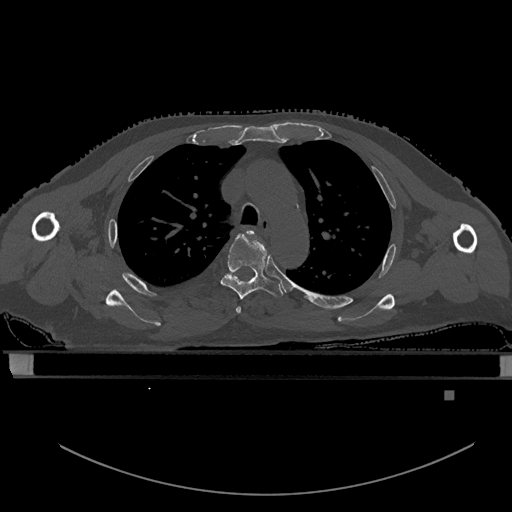
CT including the spine, one axial slice. Slice 409 of 969 in the series (ordered by position). Bone window (W 1800 / L 400 HU). 512 × 512 image matrix. Male patient, age 82 years. From the clinical record (not read from this slice): primary cancer: prostate; vertebrae with lytic lesions (as recorded): T11, T9, T8, T2.
Structures marked on this image (semi-automatic segmentation, software-assisted and operator-edited):
- T3 vertebra: bounding box [x1, y1, x2, y2] px = [235, 230, 254, 314]
- T4 vertebra: [220, 234, 283, 300]